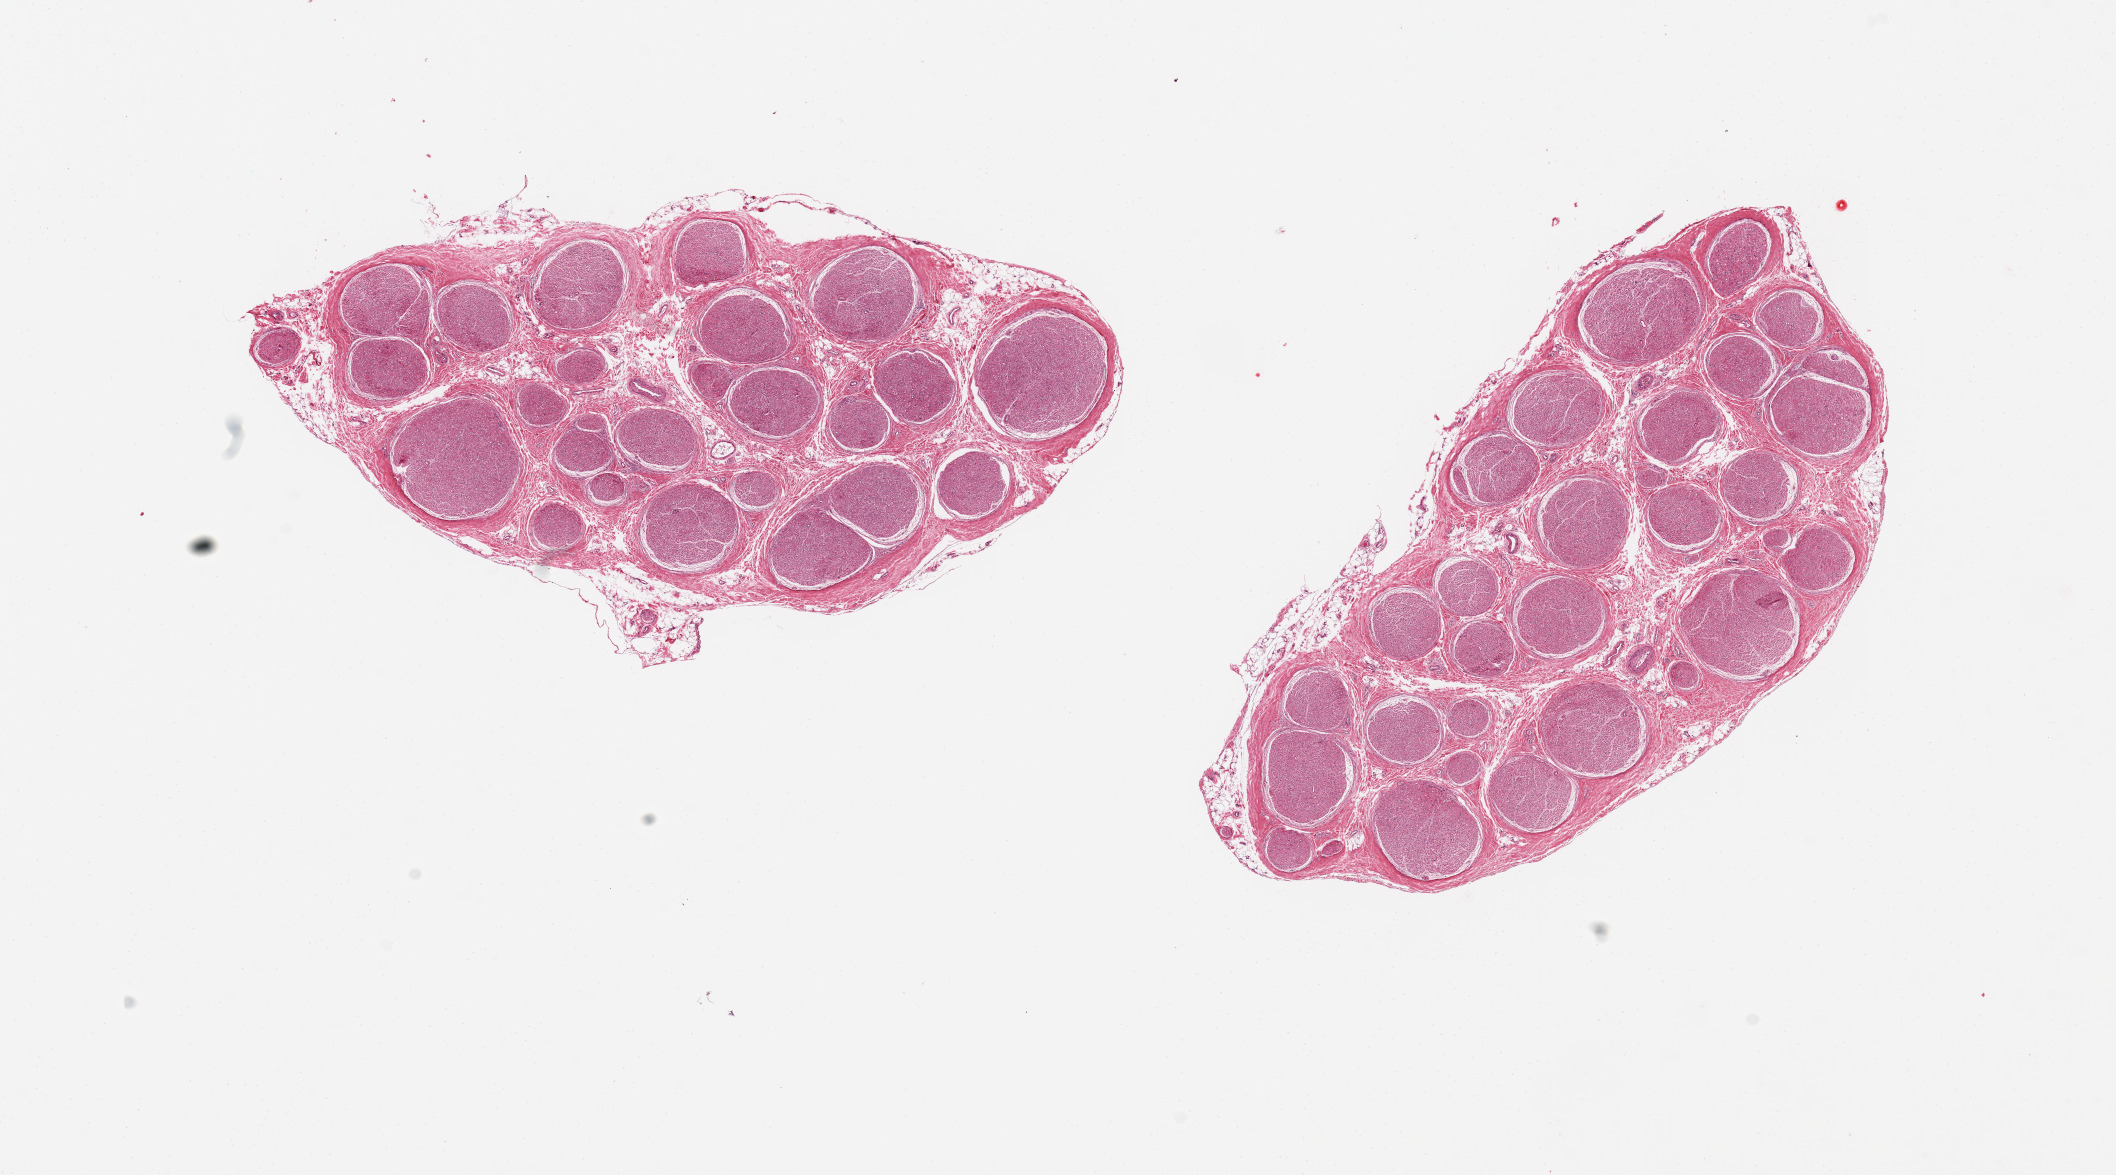
H&E whole-slide image, whole scanned area (about 16.7 x 9.3 mm) shown as a low-resolution overview. PAXgene-fixed paraffin-embedded (PFPE) section. Section of tibial nerve (target tissue). Donor tissue sample. Donor sex: male.
Reviewer comment on this tissue sample: 2 pieces , each ~6.5x3 mm.